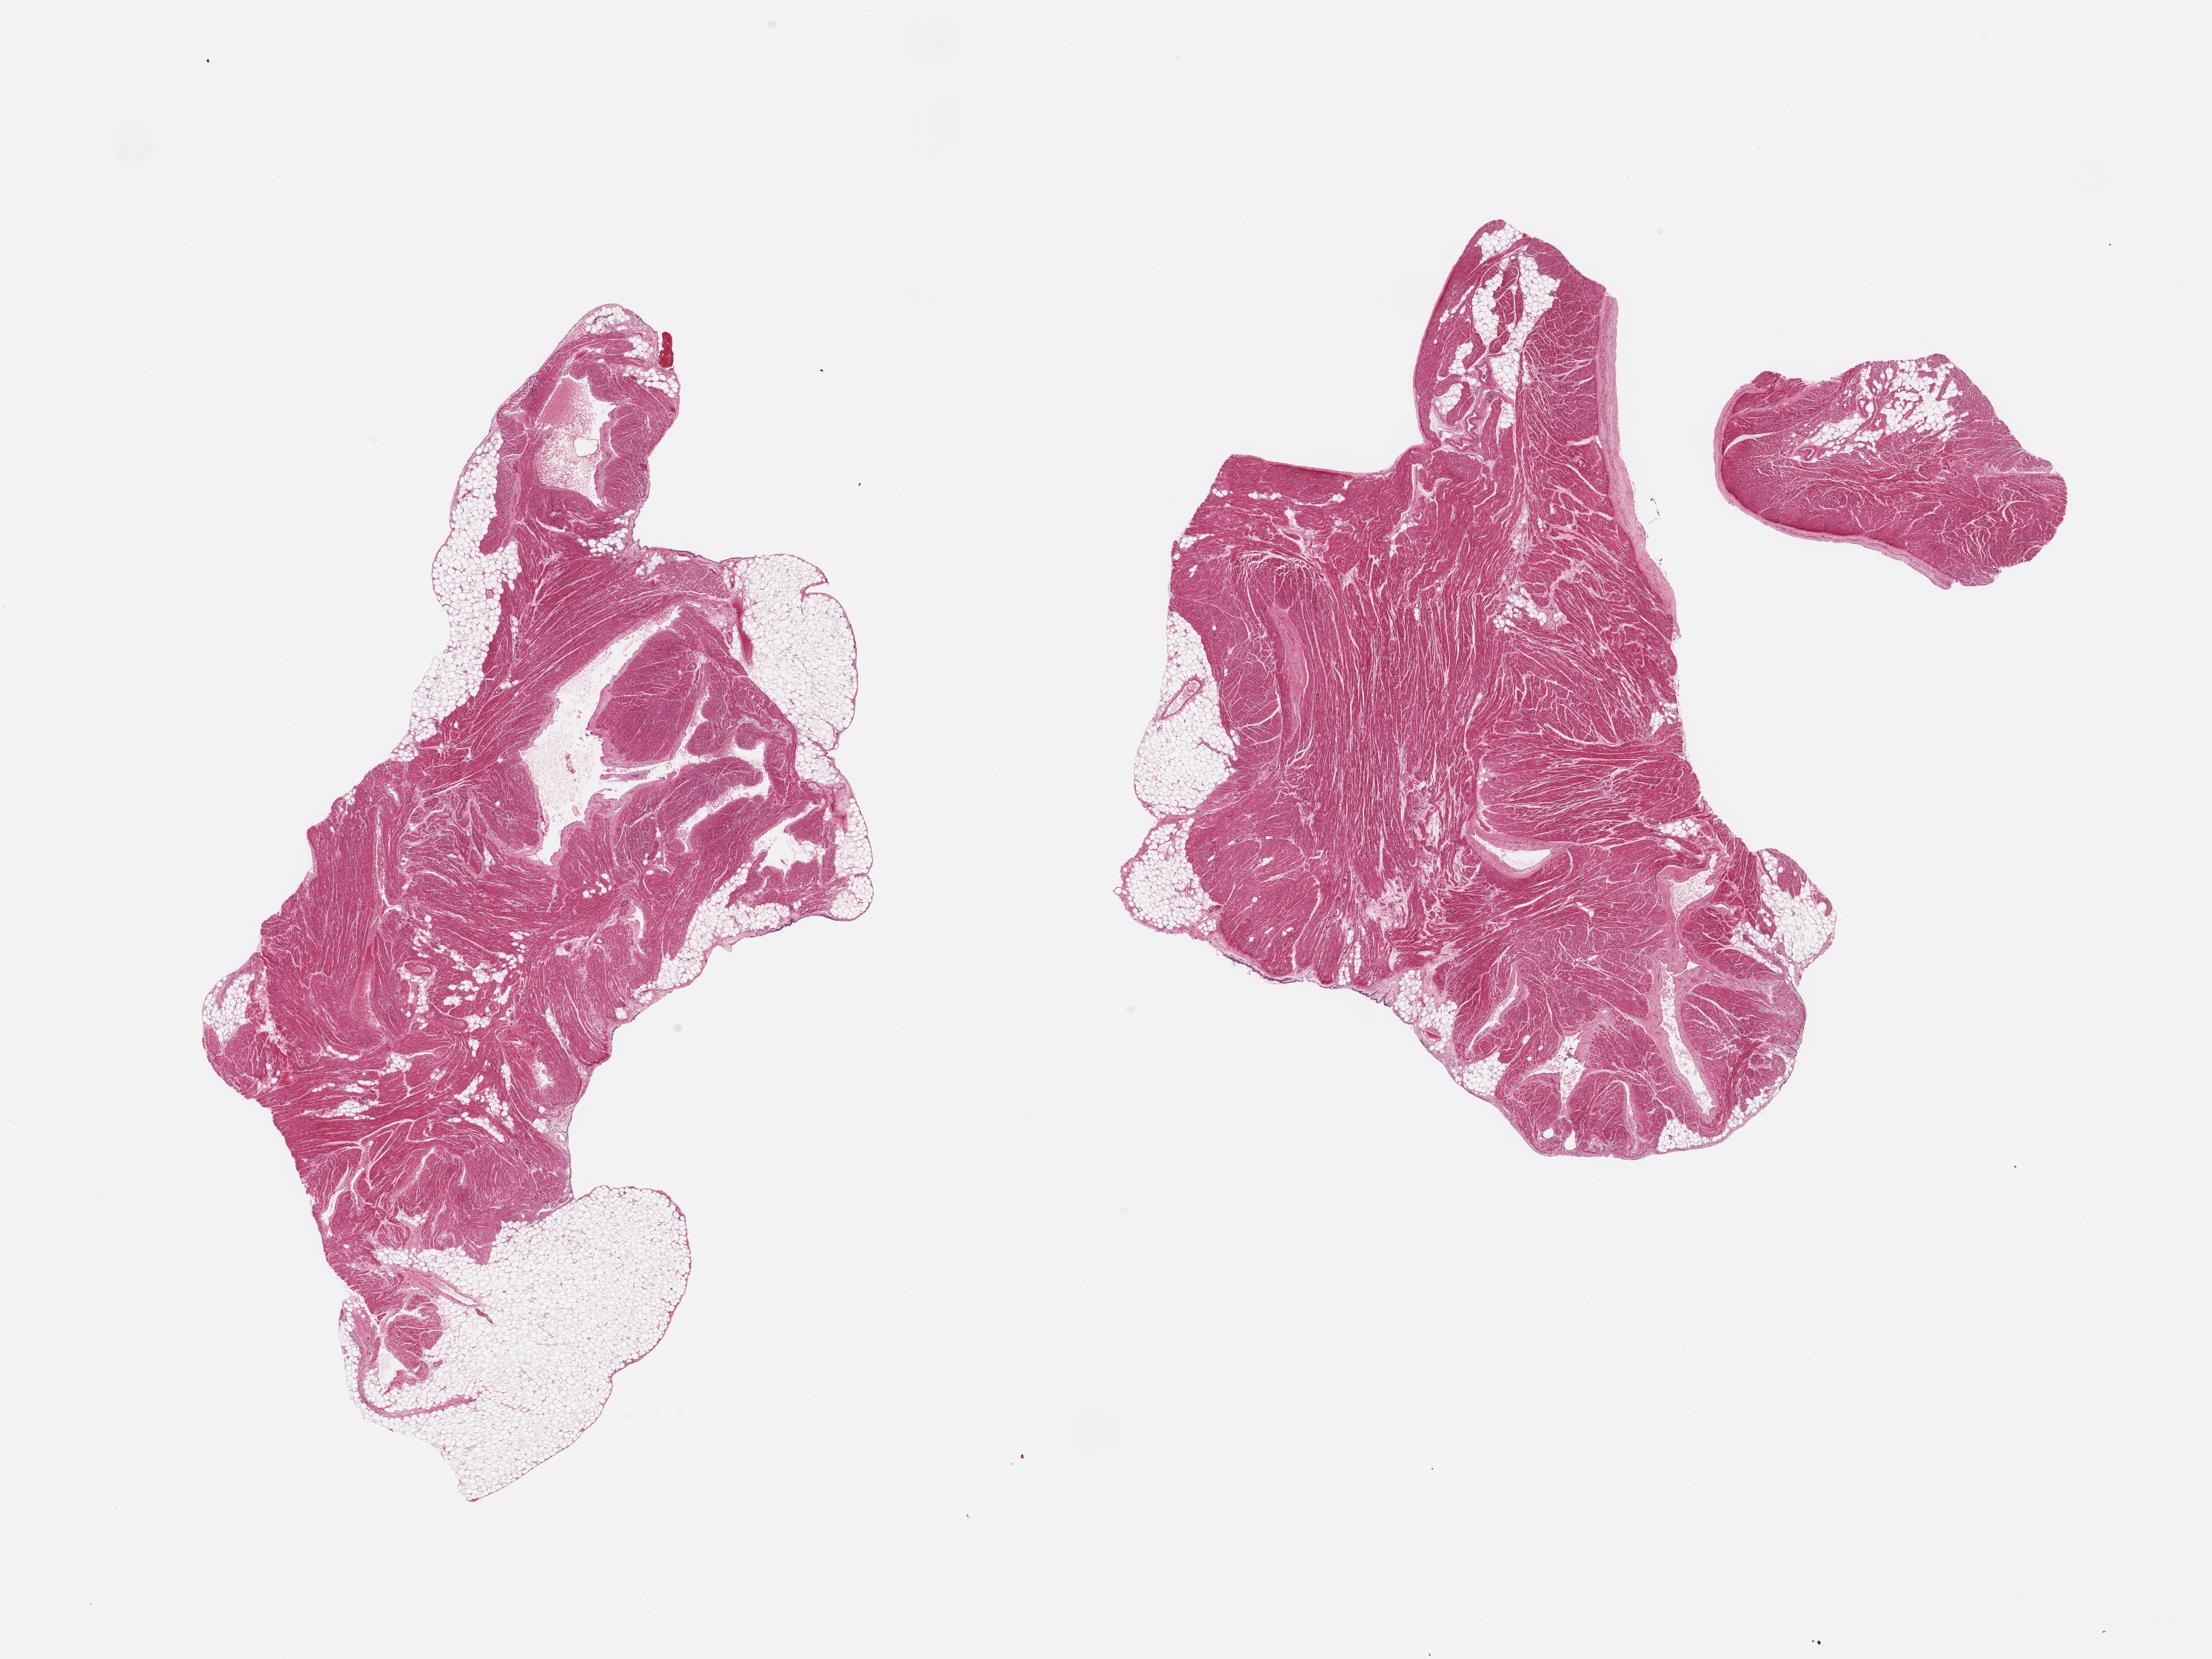
H&E whole-slide image — a low-resolution overview of the entire scanned area, about 23.6 x 17.7 mm (from a 20x scan), PAXgene-fixed, paraffin-embedded tissue, sampled site (target tissue): auricular appendage, donor tissue sample. Donor sex: female.
Pathologist's review note for this sample: 3 pieces; 10% external fat.